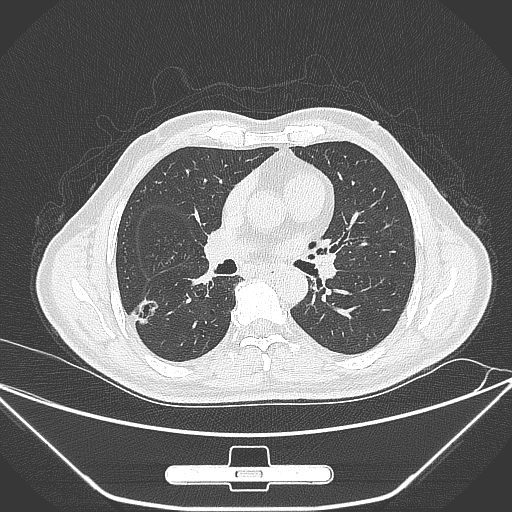
Chest CT, one axial slice. Position 154 of 310 along the scan axis. Lung window (W 1500 / L -600 HU). 512 × 512 image matrix, field of view 398 × 398 mm. Patient: male, 71 years. From the clinical record (not read from this slice): clinical TNM (as recorded): T1c N0 M0.
Annotated regions visible in this slice (rectangle marked by the reading radiologist):
- lung tumour (recorded histology: adenocarcinoma): box from (x=131, y=293) to (x=167, y=339) px